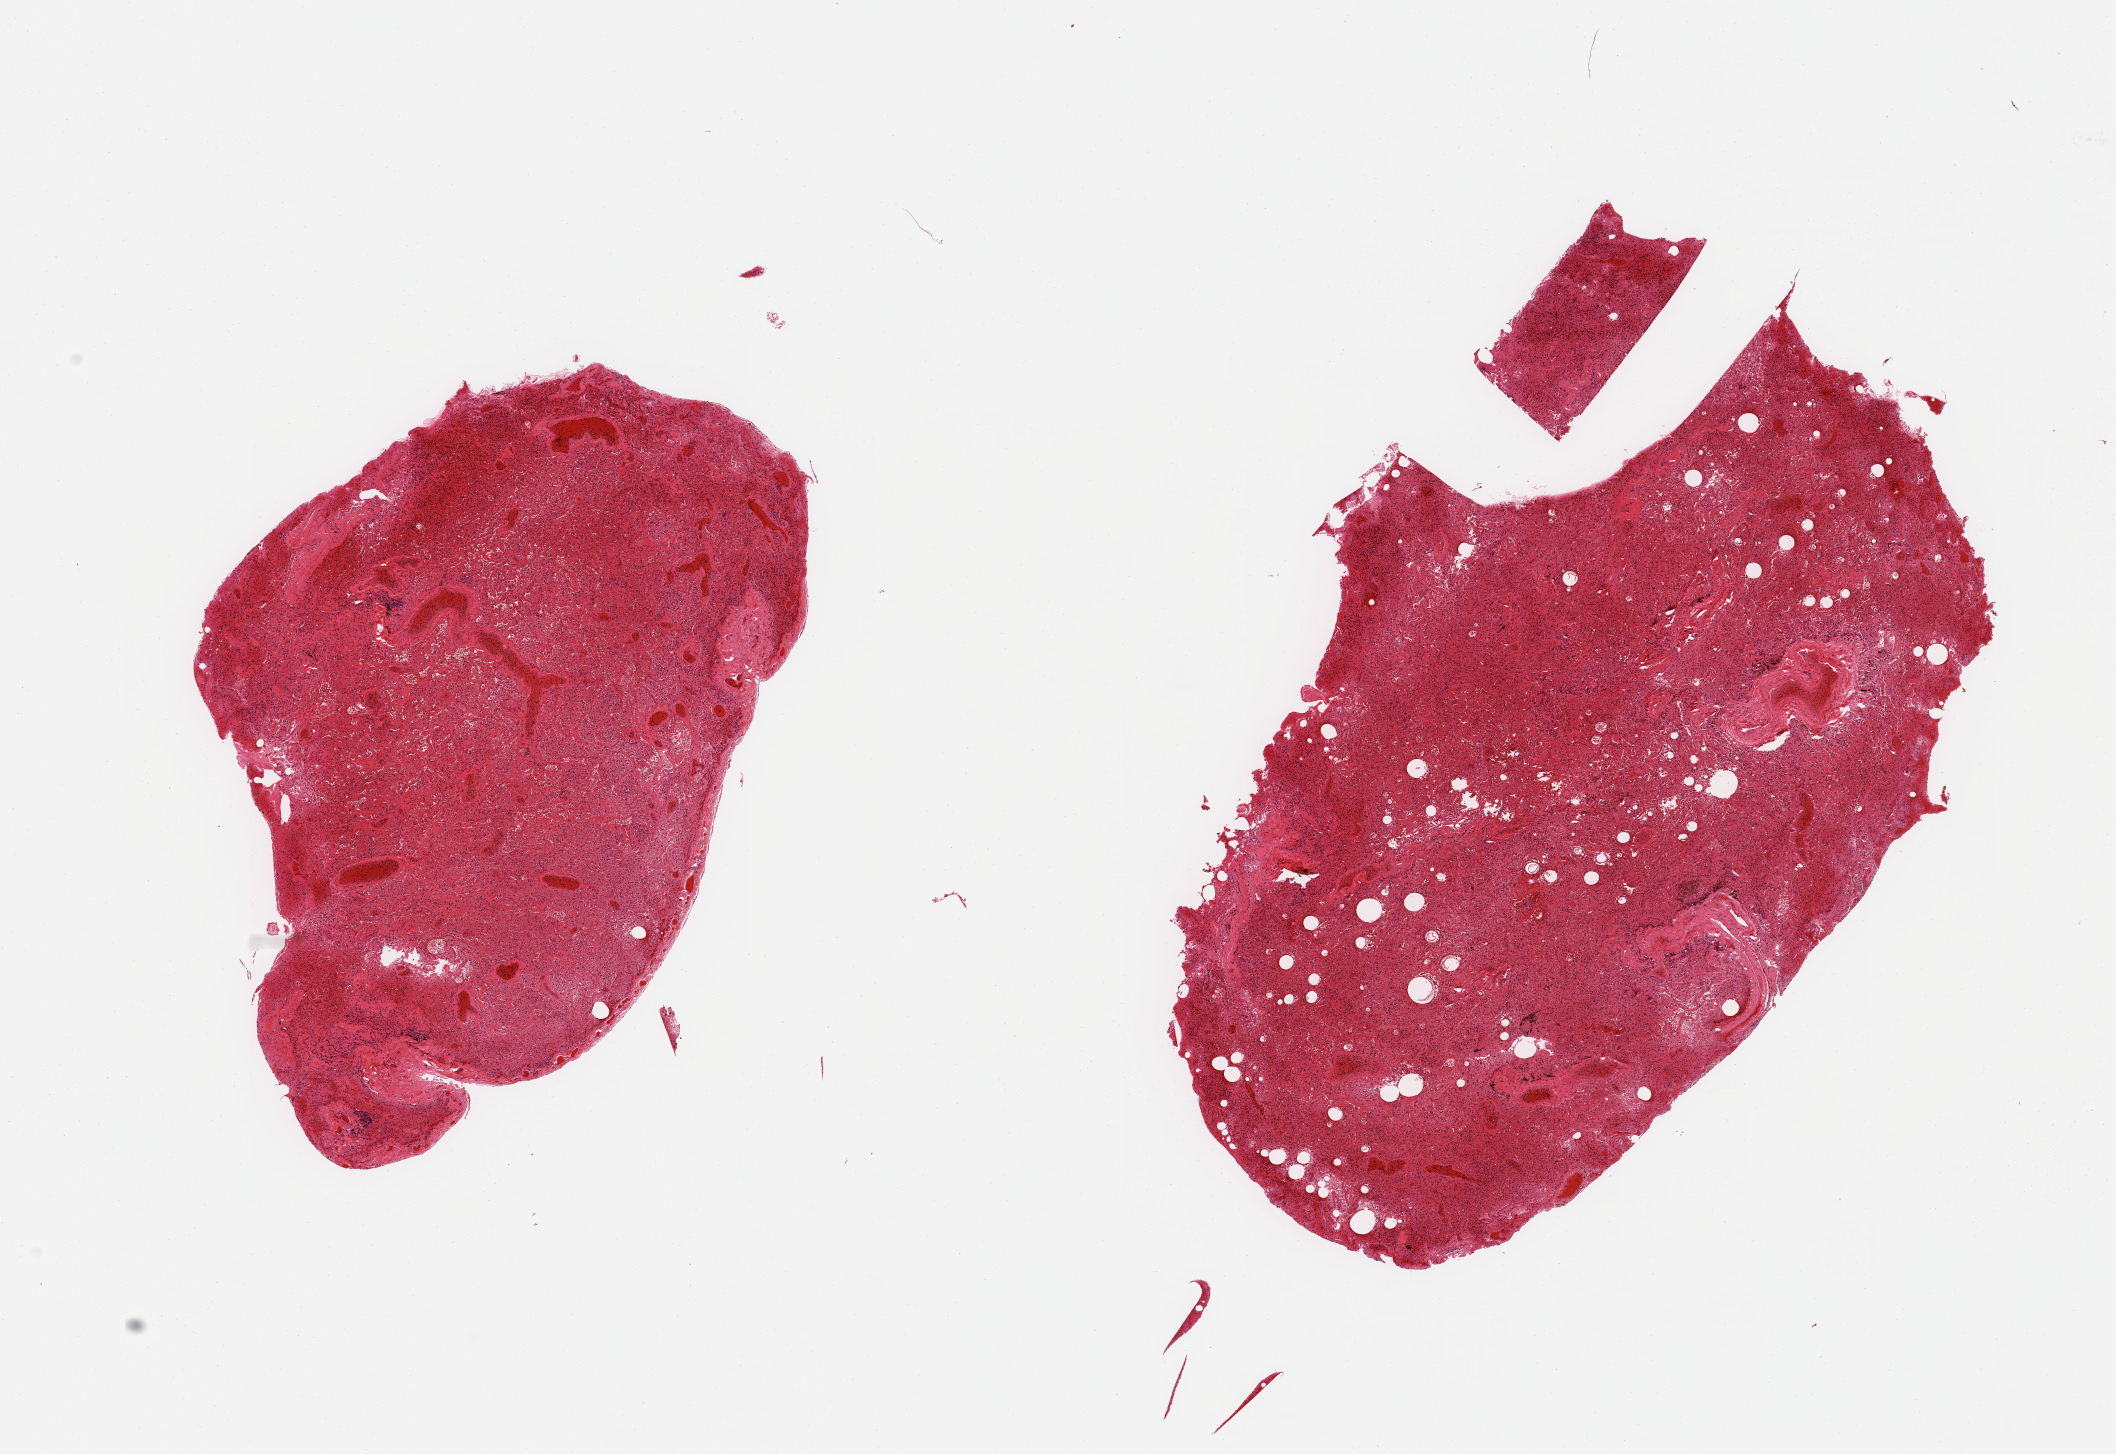
Digitized haematoxylin and eosin-stained section — low-resolution overview of the scanned area, about 16.7 x 11.5 mm (from a 20x scan), PAXgene-fixed paraffin-embedded (PFPE) section, target tissue: lung, tissue donor sample.
Review note (as recorded): 2 pieces; includes pleura (not target), severe congestion with intra-alveolar hemorrhage.